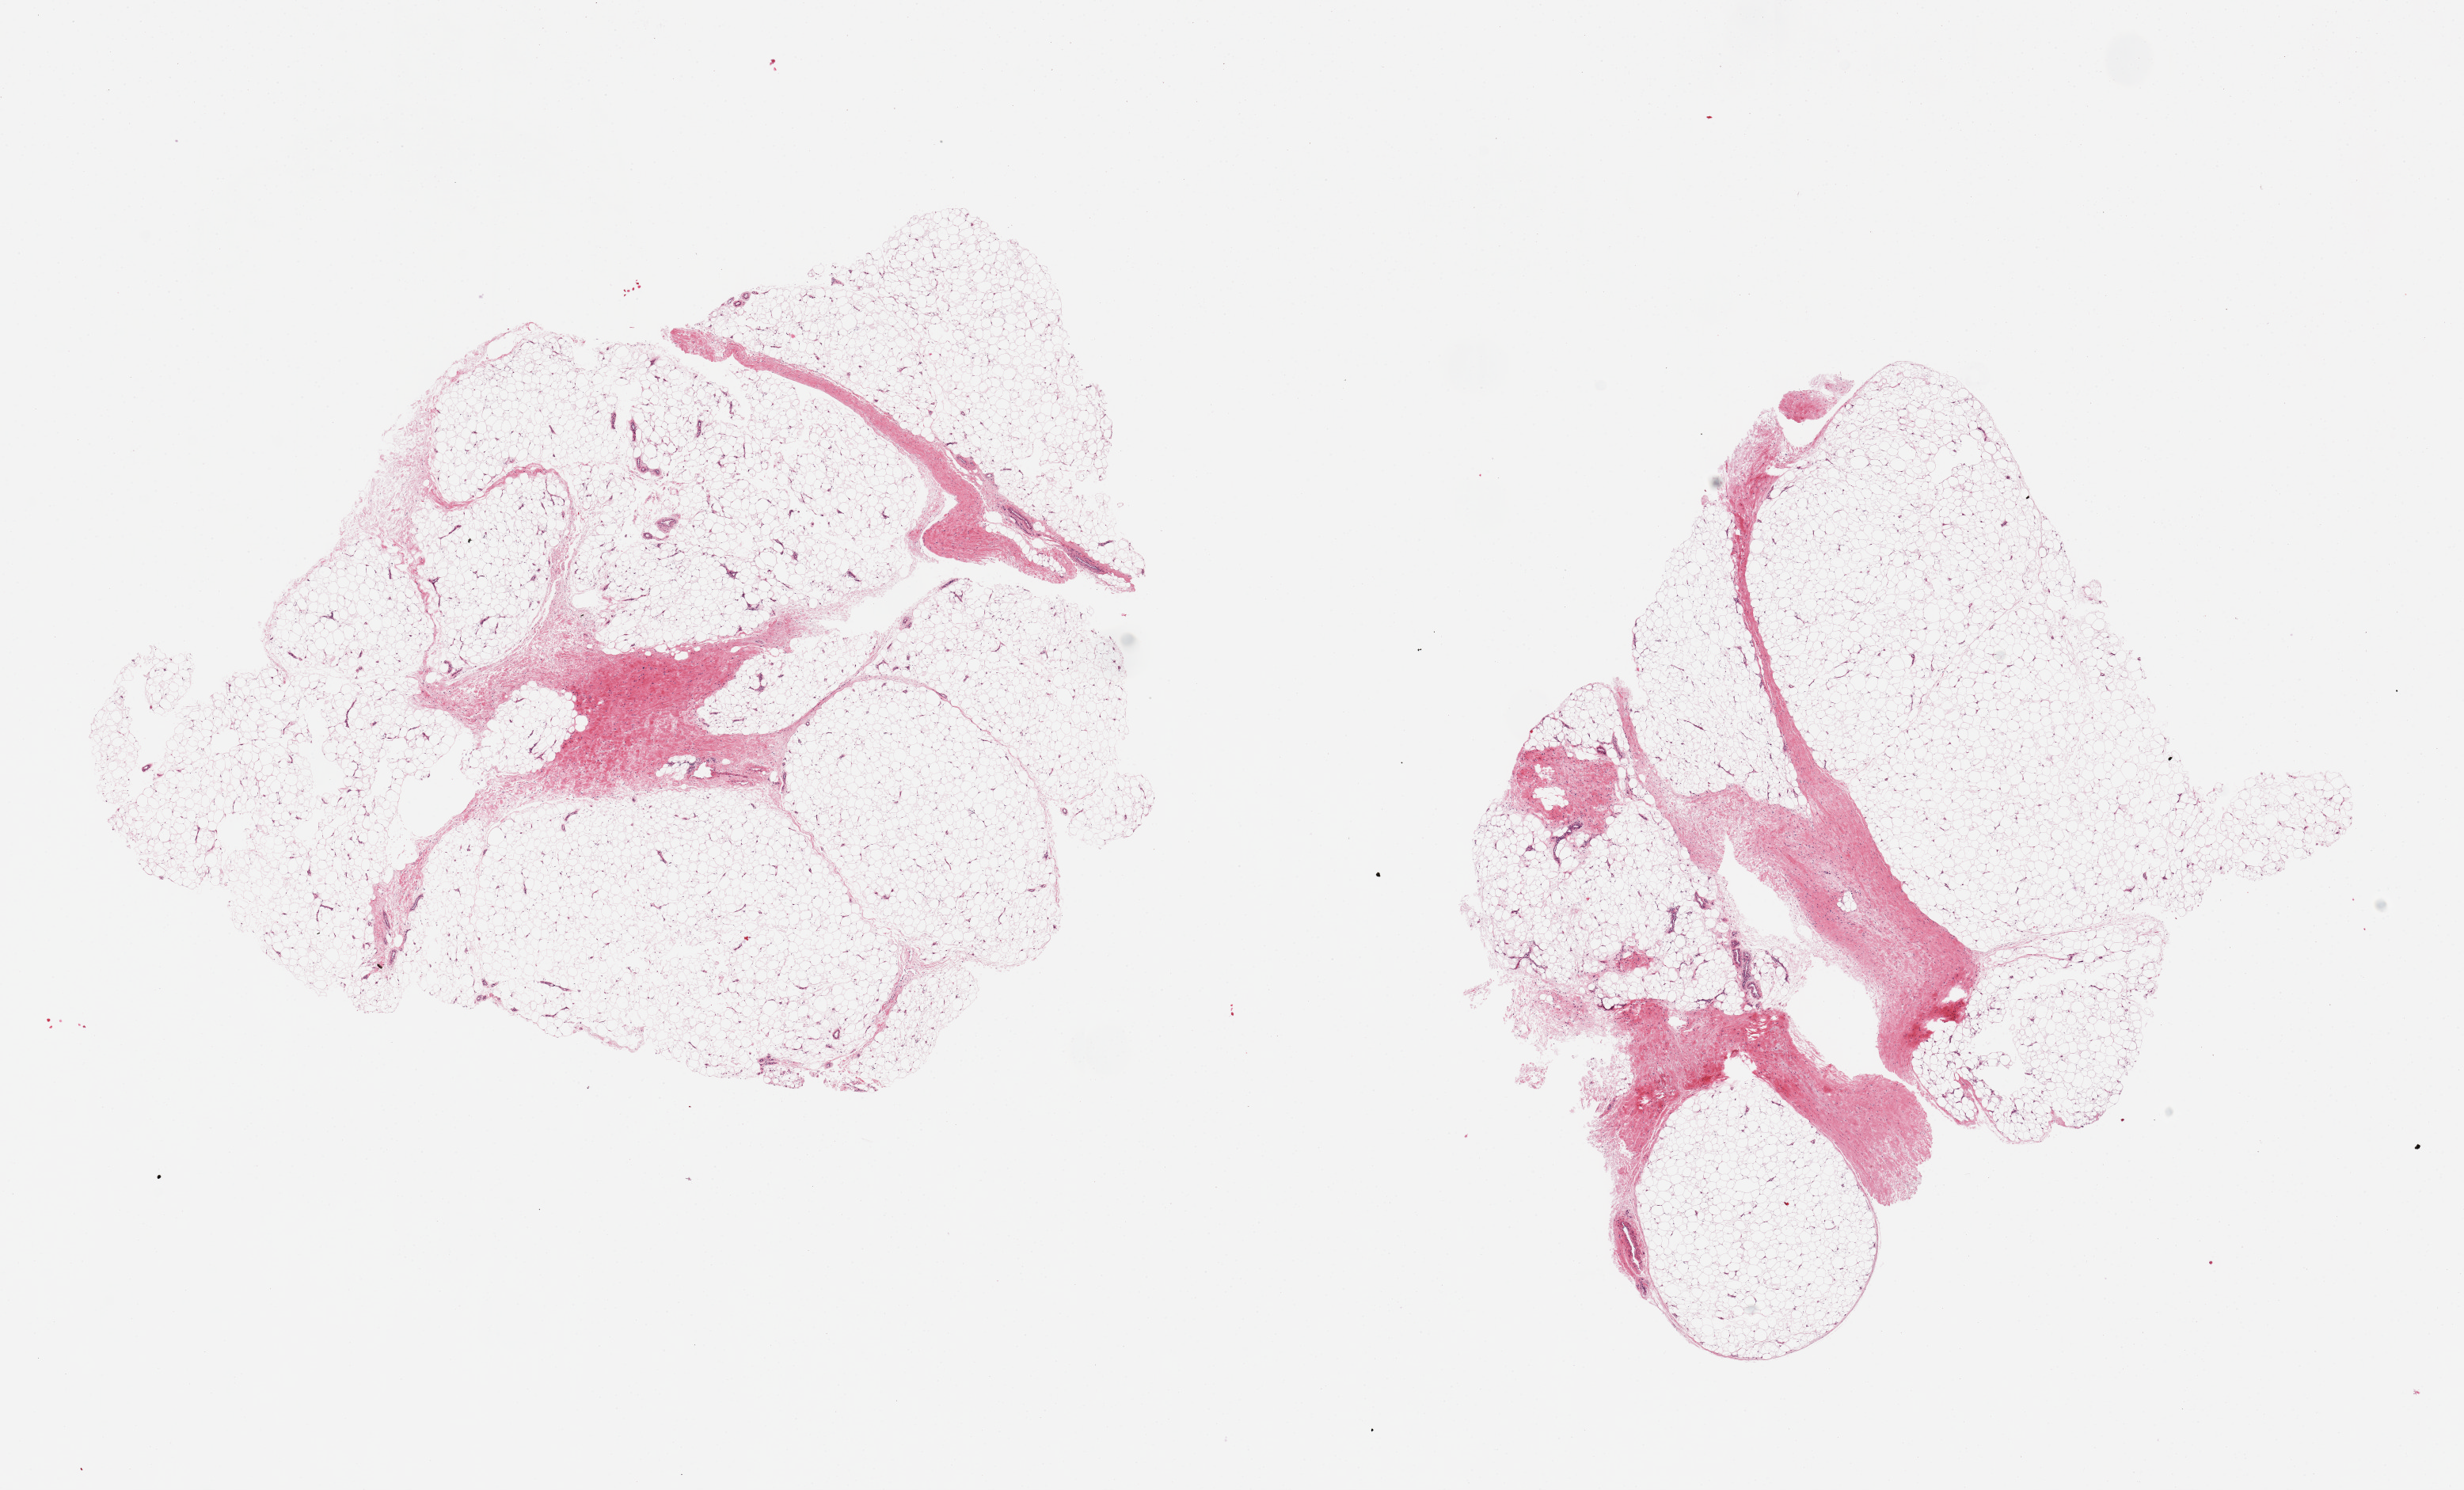
Whole-slide image, H&E stain, shown as a low-resolution overview of the whole scanned area (about 24.6 x 14.9 mm, acquisition: 20x scan), PAXgene-fixed, paraffin-embedded tissue, sampled site (target tissue): adipose tissue, donor tissue sample. Male donor.
Review note (as recorded): 2 pieces. 10% fibrous tissue admixed.